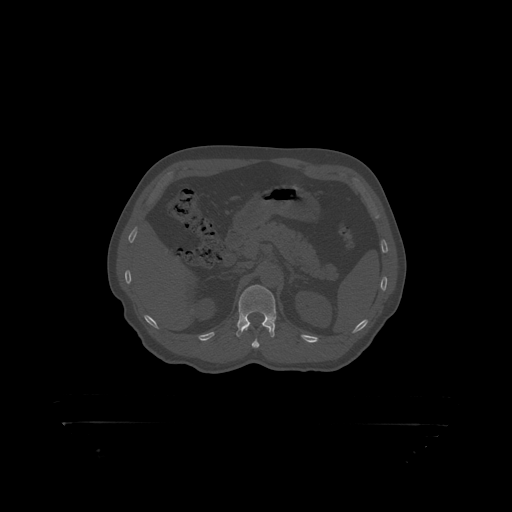
CT including the spine, one axial slice; slice 333 of 399 in the series (ordered by position); 120 kVp; bone window (W 1800 / L 400 HU); 1.25 mm slice thickness; 512 × 512 image matrix, field of view 650 × 650 mm. Male patient, age 46 years. Case-level facts recorded for this patient, not image findings: primary cancer: skin.
Annotated regions visible in this slice (semi-automatic segmentation, software-assisted and operator-edited):
- L1 vertebra: bounding box [x1, y1, x2, y2] px = [239, 285, 277, 319]